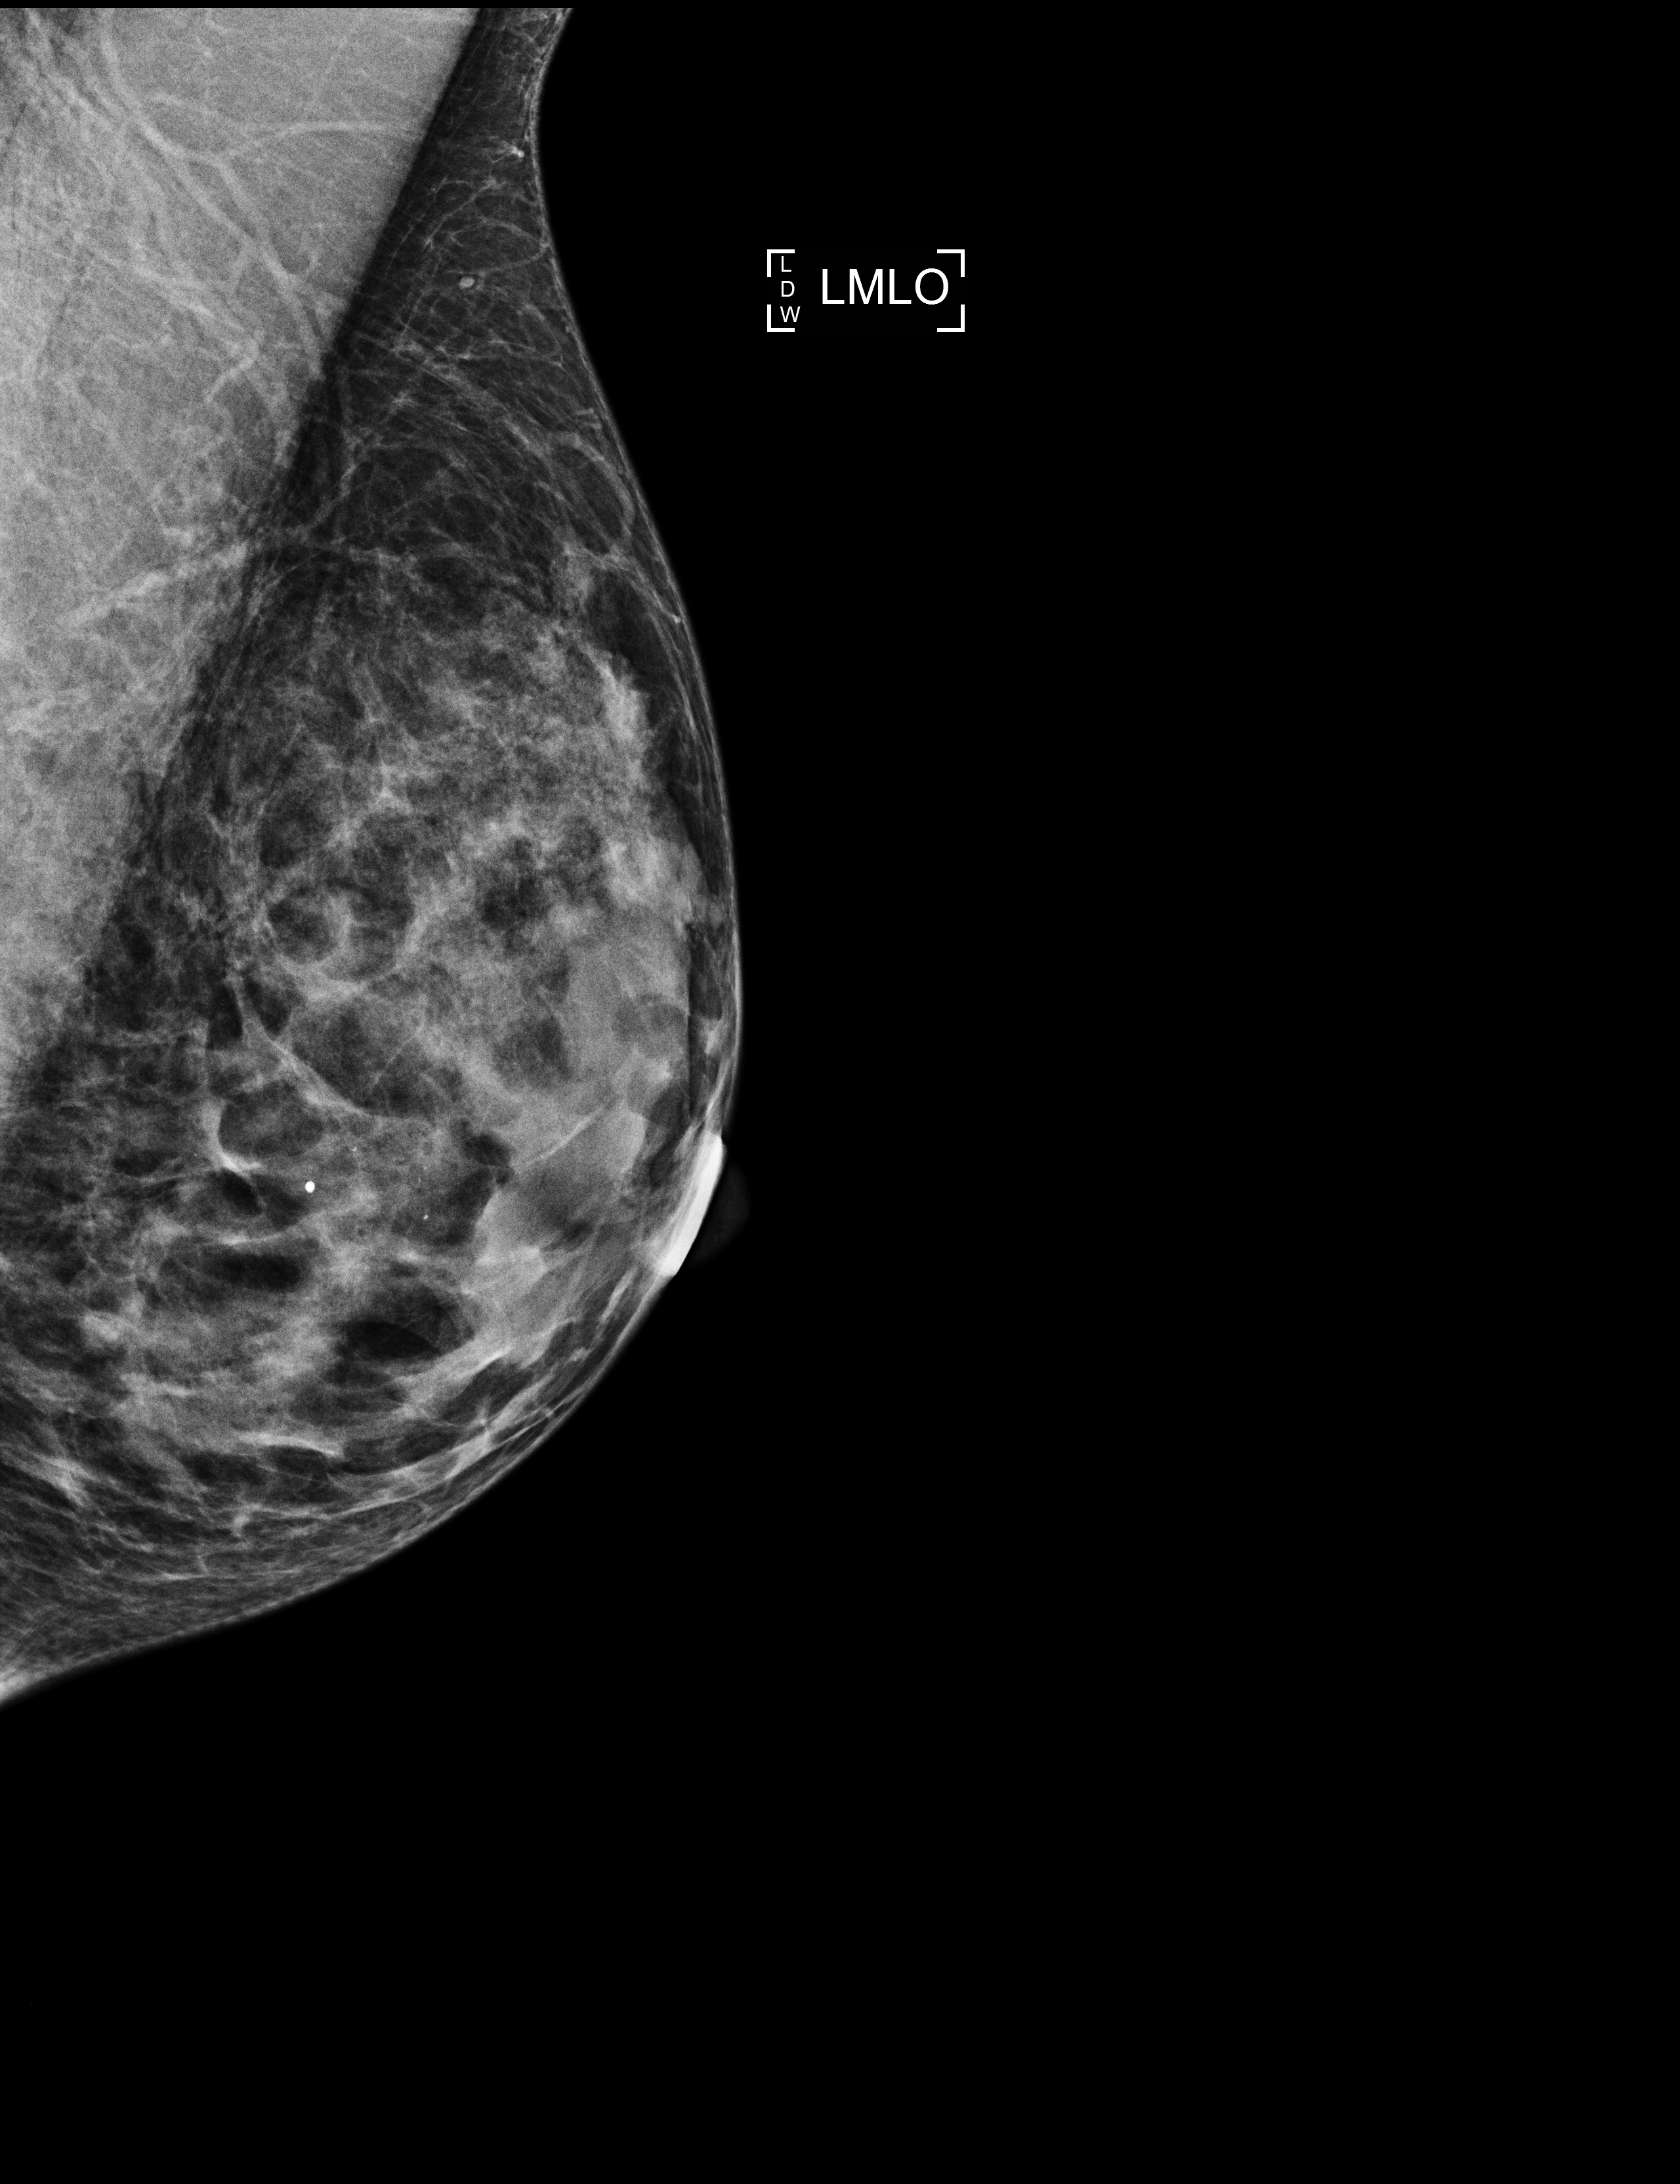
Digital mammogram (FFDM); left breast; medio-lateral oblique projection; screening examination. Patient aged 58 years (female).
BI-RADS breast density category at the screening exam (both breasts, scale 1–4): 3. Final BI-RADS category for the screening round (tomosynthesis exam, both breasts): category 2. Recall: no recall after this screen.